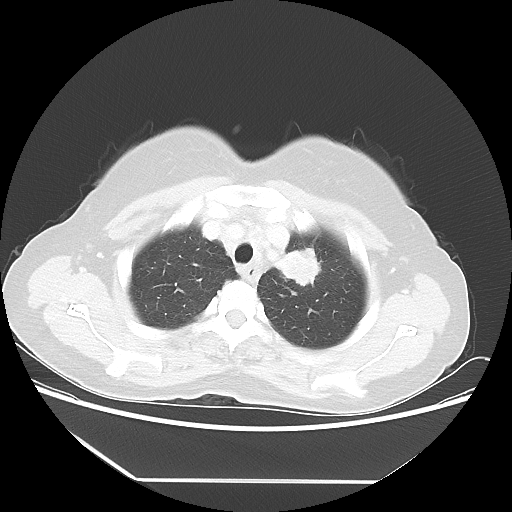
Chest CT, one axial slice. Position 44 of 52 along the scan axis. Reconstruction kernel LUNG. 100 kVp. Lung window (W 1500 / L -600 HU). 5 mm slice thickness. 512 × 512 image matrix, field of view 390 × 390 mm. Patient: female, 50 years. From the clinical record (not read from this slice): clinical TNM (as recorded): T2 N3 M0.
Annotated regions visible in this slice (rectangle marked by the reading radiologist):
- lung tumour (recorded histology: adenocarcinoma): bounding box <269,239,326,295> (left, top, right, bottom; pixels)